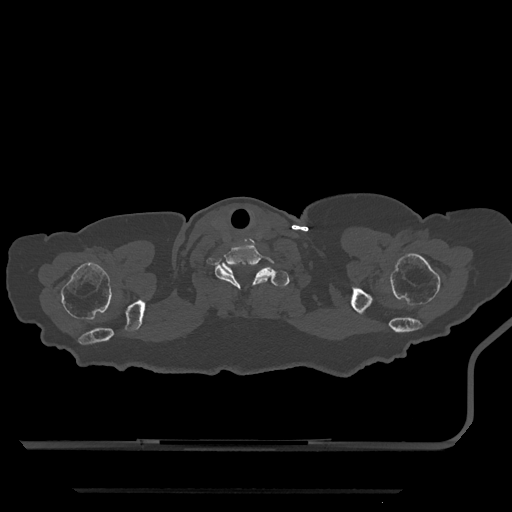
CT including the spine, one axial slice; slice 731 of 797 in the series (ordered by position); bone window (W 1800 / L 400 HU); 512 × 512 image matrix, field of view 440 × 440 mm. Patient: female, 51 years. From the clinical record (not read from this slice): primary cancer: neuro; vertebrae with lytic lesions (as recorded): T8.
Outlined on this slice (semi-automatically segmented with operator editing):
- T1 vertebra: bounding box [x1, y1, x2, y2] px = [222, 263, 290, 287]